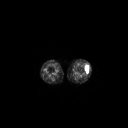
FDG PET of an extremity soft-tissue mass (from a PET/CT study), one axial slice. Slice 168 of 223 in the series (ordered by position). 3.27 mm slice thickness. 128 × 128 image matrix, field of view 700 × 700 mm. Patient: female, 16 years. From the clinical record (not read from this slice): histological type: spindle cell suggestive of biphasic synovial sarcoma; grade: intermediate; site of the primary tumour: left knee.
Annotated regions visible in this slice (expert contour drawn on MRI and transferred to this co-registered scan by the dataset authors):
- gross tumour volume including surrounding oedema: box from (x=85, y=65) to (x=89, y=73) px
- gross tumour volume (mass): (x=85, y=66)–(x=89, y=73)